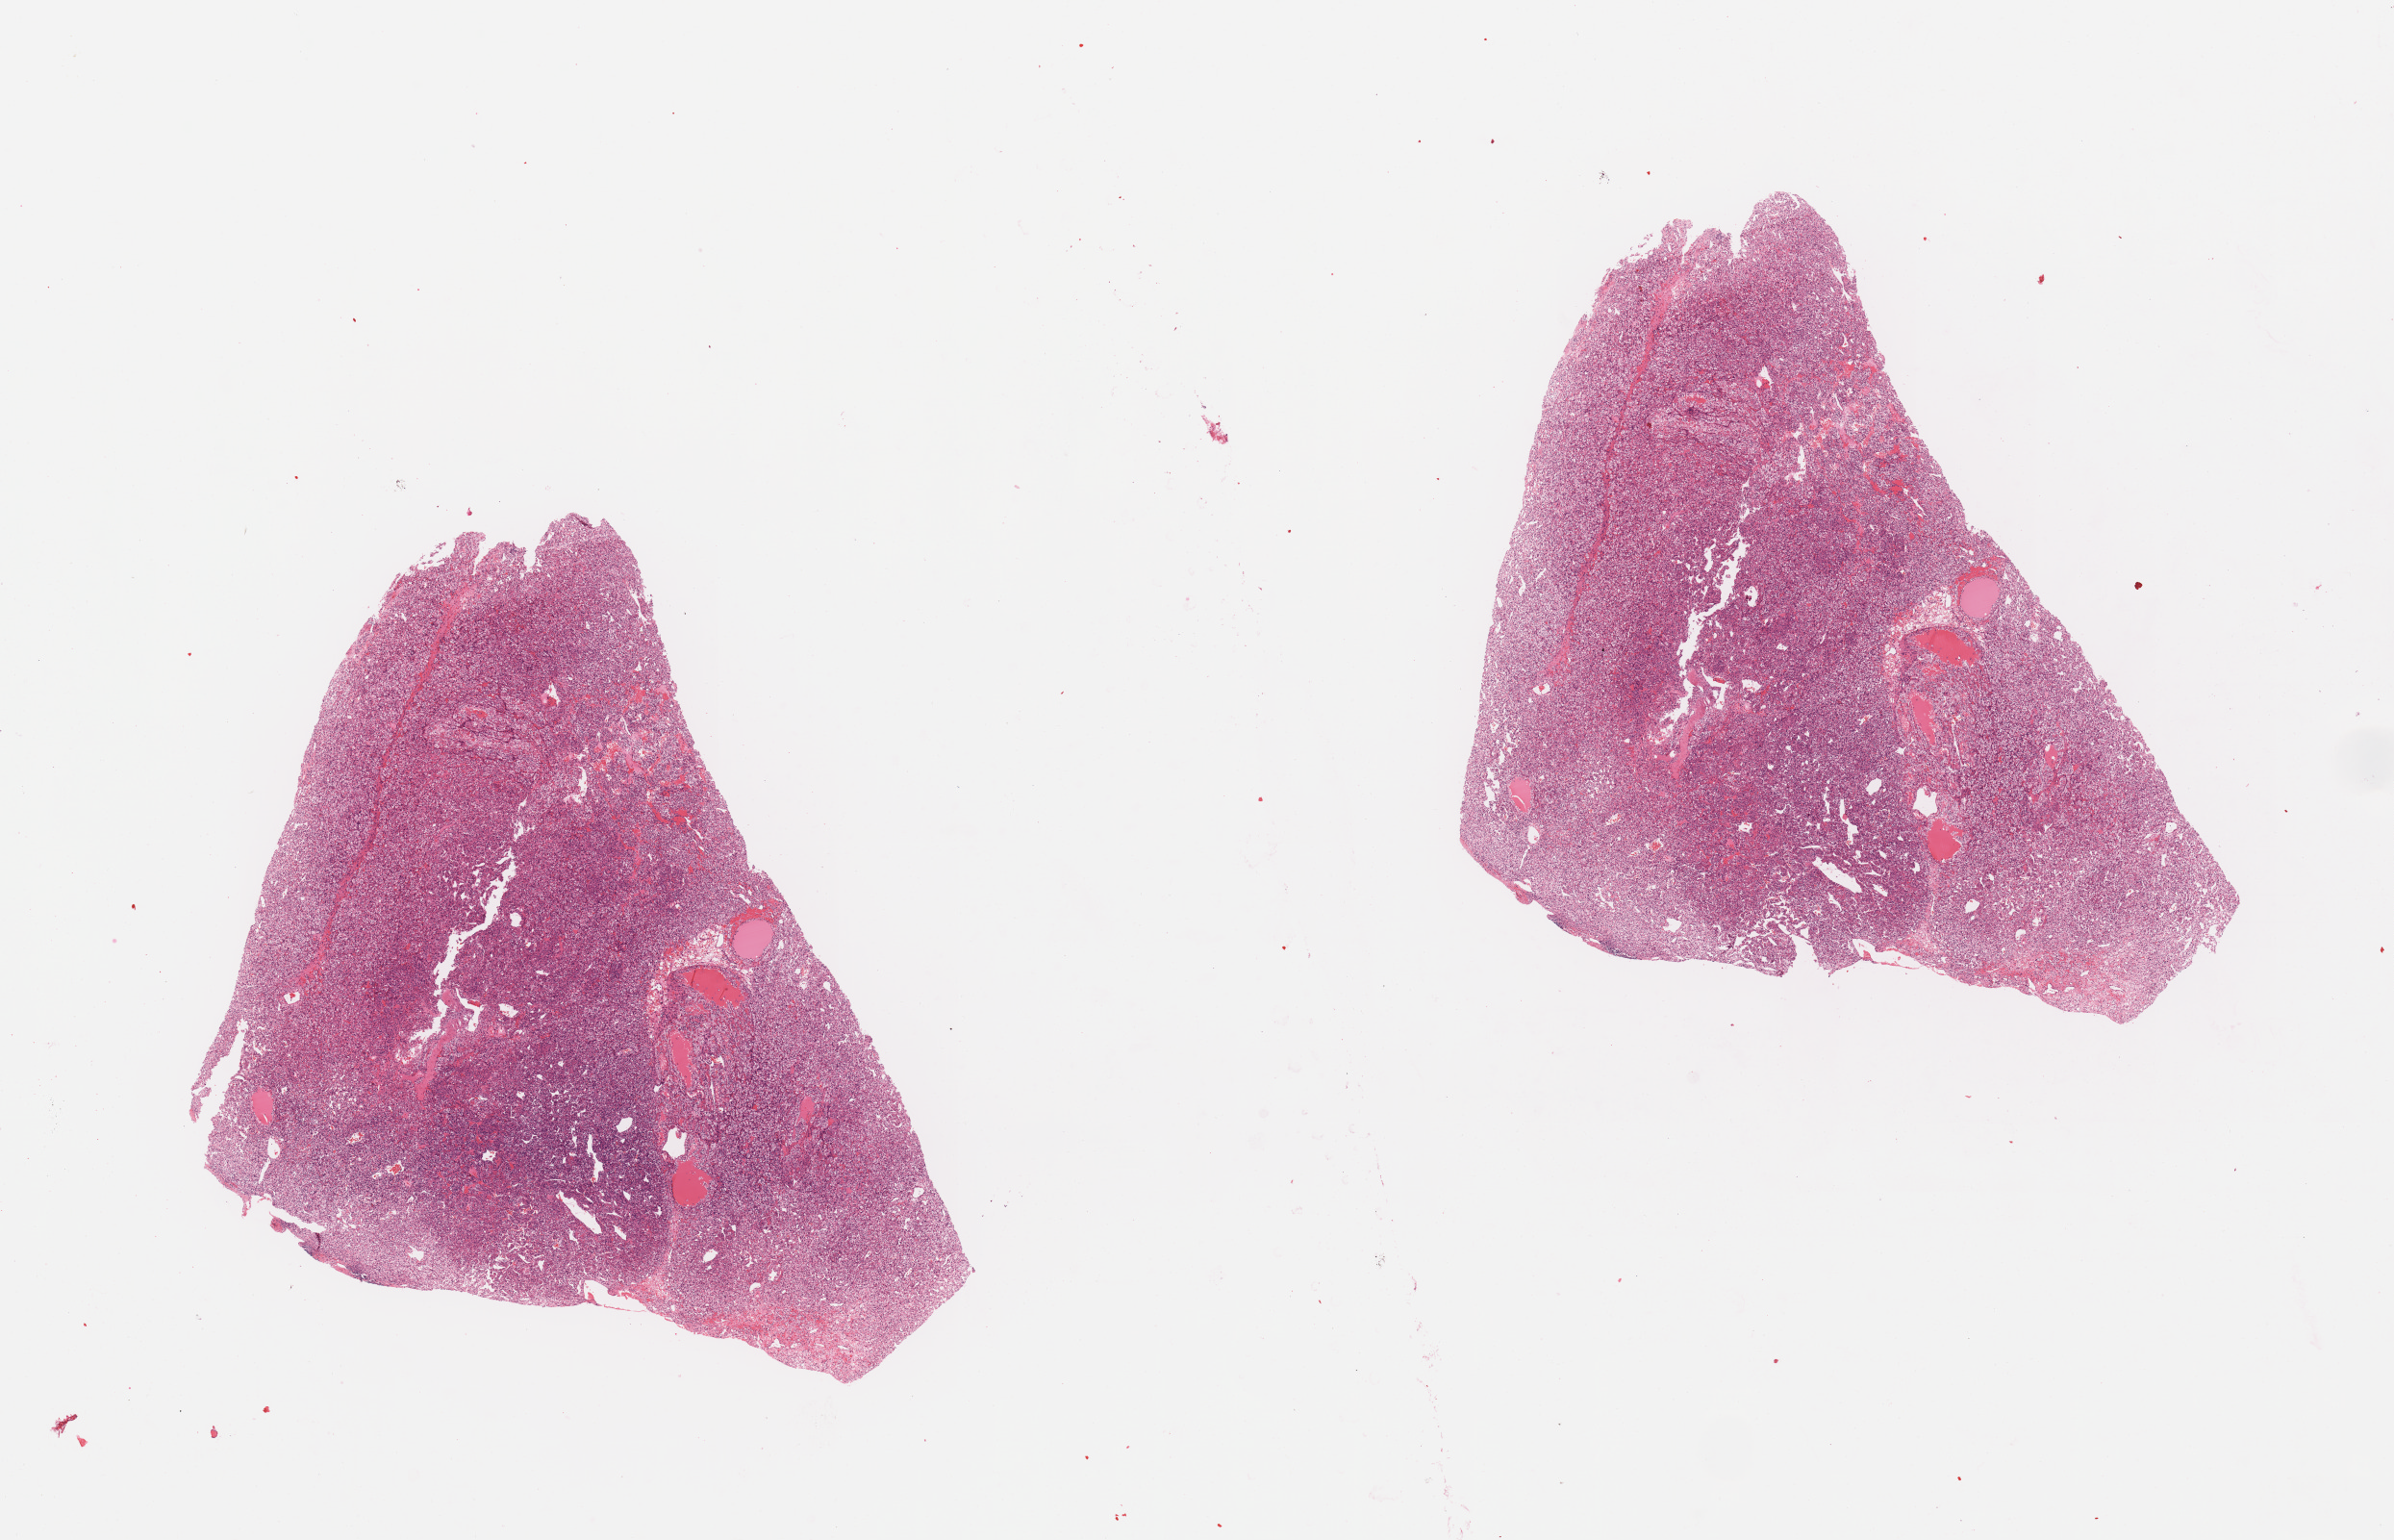
Digitized H&E-stained tissue section (whole slide) — a low-resolution overview of the entire scanned area, about 19.7 x 12.7 mm; tumour tissue sample, sampled site: kidney. 52-year-old male patient.
Histologic diagnosis: Renal cell carcinoma, NOS.